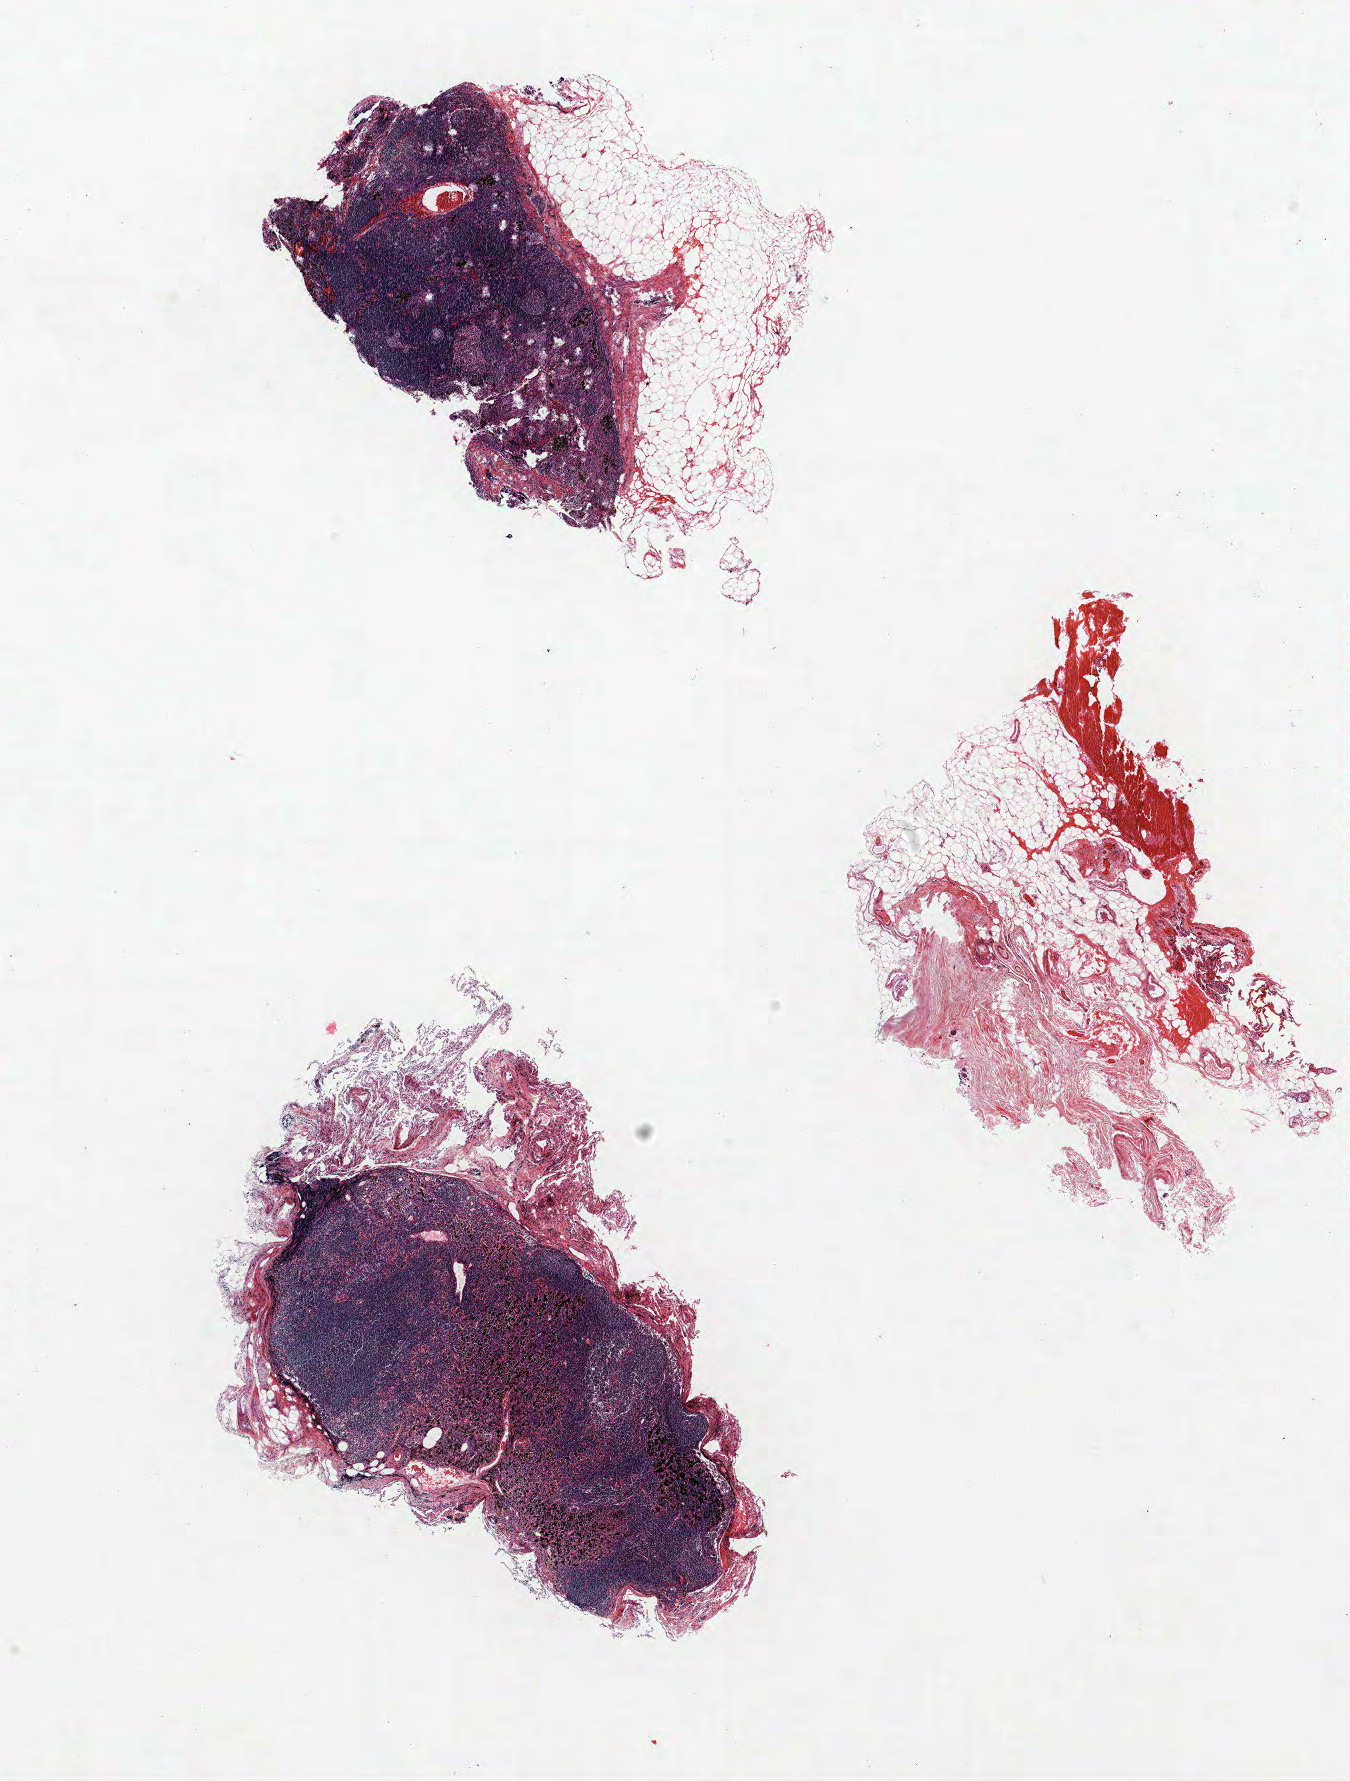
Whole-slide histology image, H&E, shown as a low-resolution overview of the whole scanned area (about 10.8 x 14.3 mm, acquisition: 40x scan), formalin-fixed paraffin-embedded (FFPE) section, lung tissue. Male, age 65 at enrolment. Former smoker at enrolment. Grade: moderately differentiated (G2).
Stage (AJCC 6th edition): IA. Participant's lung-cancer diagnosis: Adenocarcinoma, NOS. Tumour size (pathology): 11 mm. Primary tumour location (clinical record): right upper lobe.